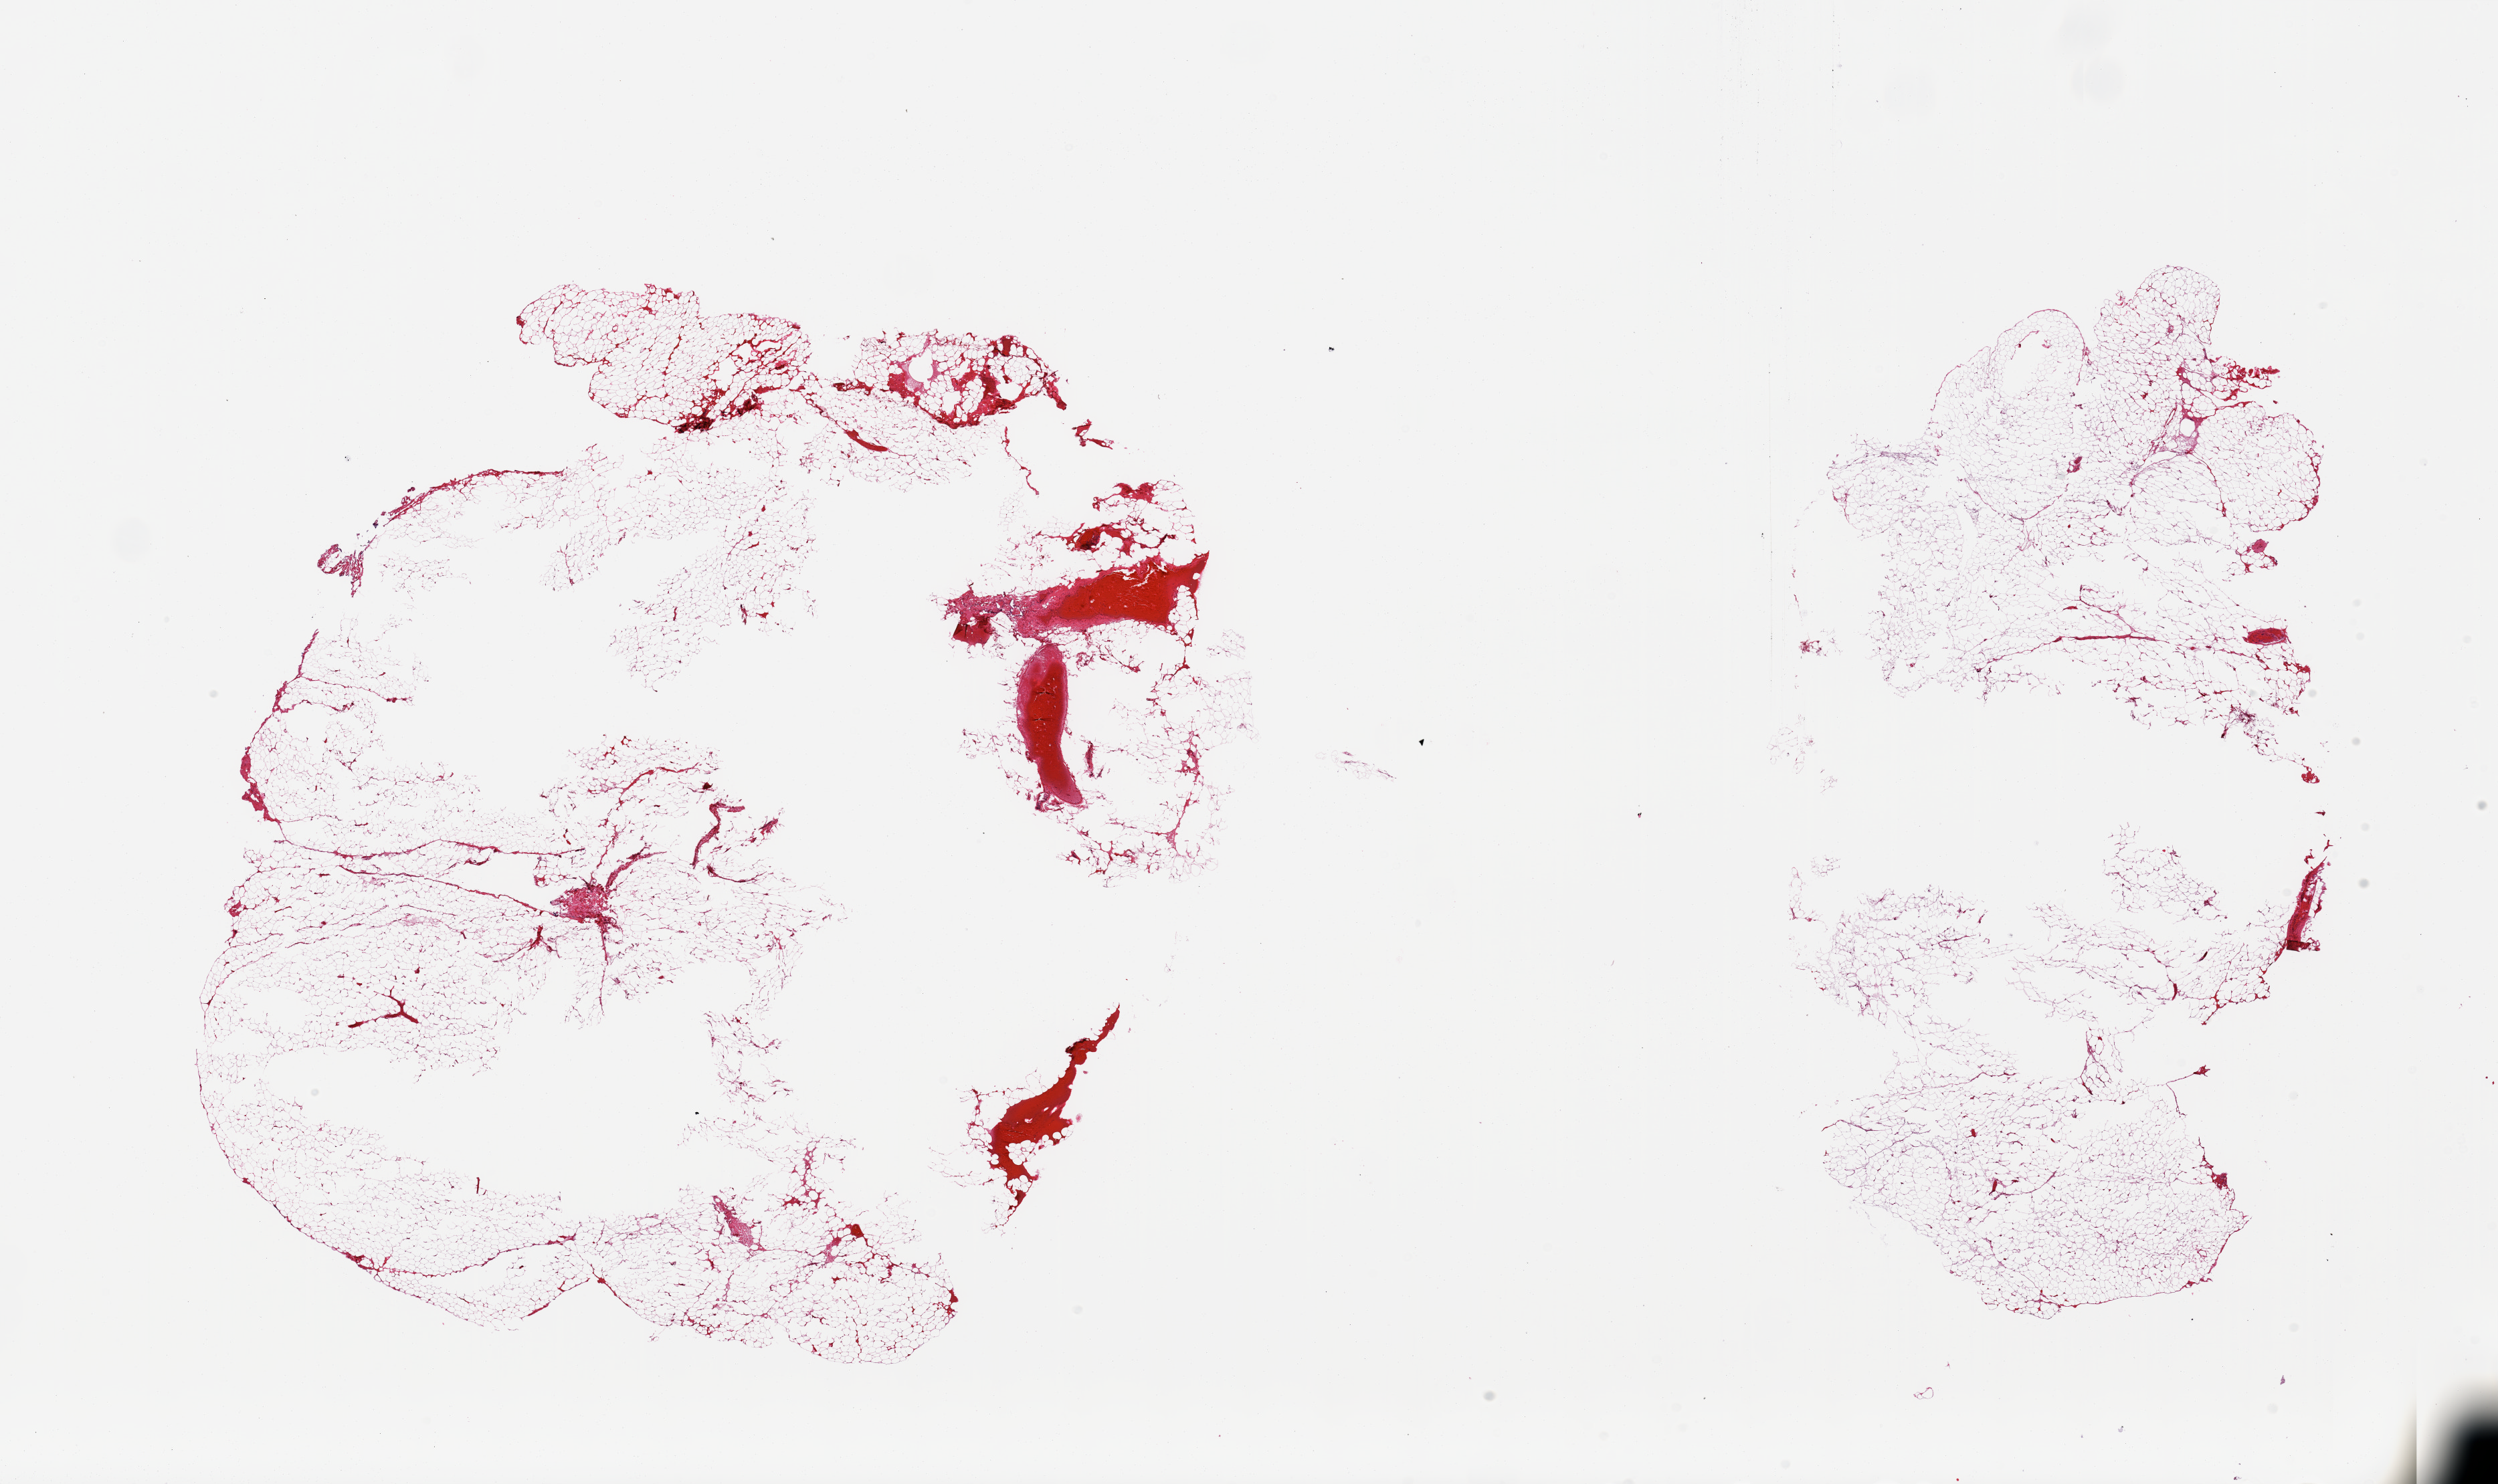
Hematoxylin and eosin (H&E) whole-slide image, brightfield — whole scanned area (about 29.5 x 17.6 mm) shown as a low-resolution overview; PAXgene-fixed, paraffin-embedded tissue; target tissue: adipose tissue; tissue donor sample.
Reviewer comment on this tissue sample: 2 pieces, ~10% fascia.